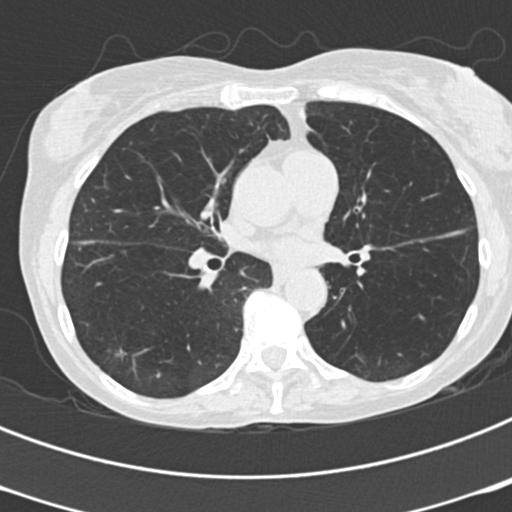
Low-dose screening chest CT, axial slice; third screening round (two years after baseline); lung window (W 1500 / L -600 HU); 2 mm slice thickness; 120 kVp. Female participant, aged 68 years at enrolment. Former smoker at enrolment.
- Expert reader's lesion annotation, box from (x=102, y=333) to (x=141, y=365) px.
- Reader record for this screening exam (exam-level; its link to the box is not recorded): non-calcified nodule or mass ≥4 mm, right lower lobe, 9 × 5 mm, poorly defined margins, soft tissue attenuation, pre-existing on the prior screen: yes; interval growth: no.
- Later outcome: lung cancer diagnosed 310 days after this screen — squamous cell carcinoma, NOS, right lower lobe, stage IA (AJCC 6th edition).